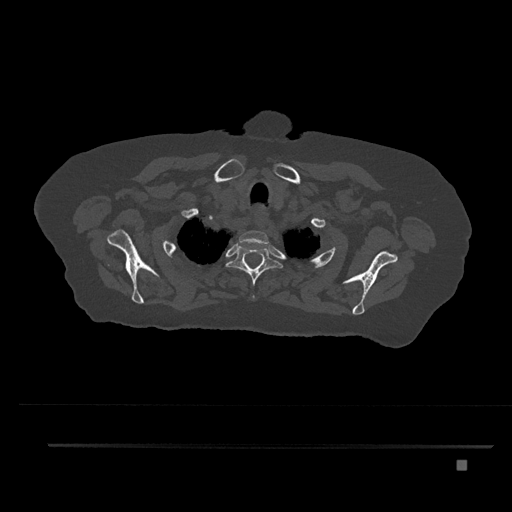
CT including the spine, one axial slice. Position 674 of 797 along the scan axis. Reconstruction kernel Br40s/3. Bone window (W 1800 / L 400 HU). 0.5 mm slice thickness. 512 × 512 image matrix. Female patient, age 76 years. Case-level facts recorded for this patient, not image findings: primary cancer: lung.
Outlined on this slice (semi-automatically segmented with operator editing):
- T1 vertebra: box from (x=239, y=231) to (x=269, y=247) px
- T2 vertebra: (x=225, y=243)–(x=283, y=299)